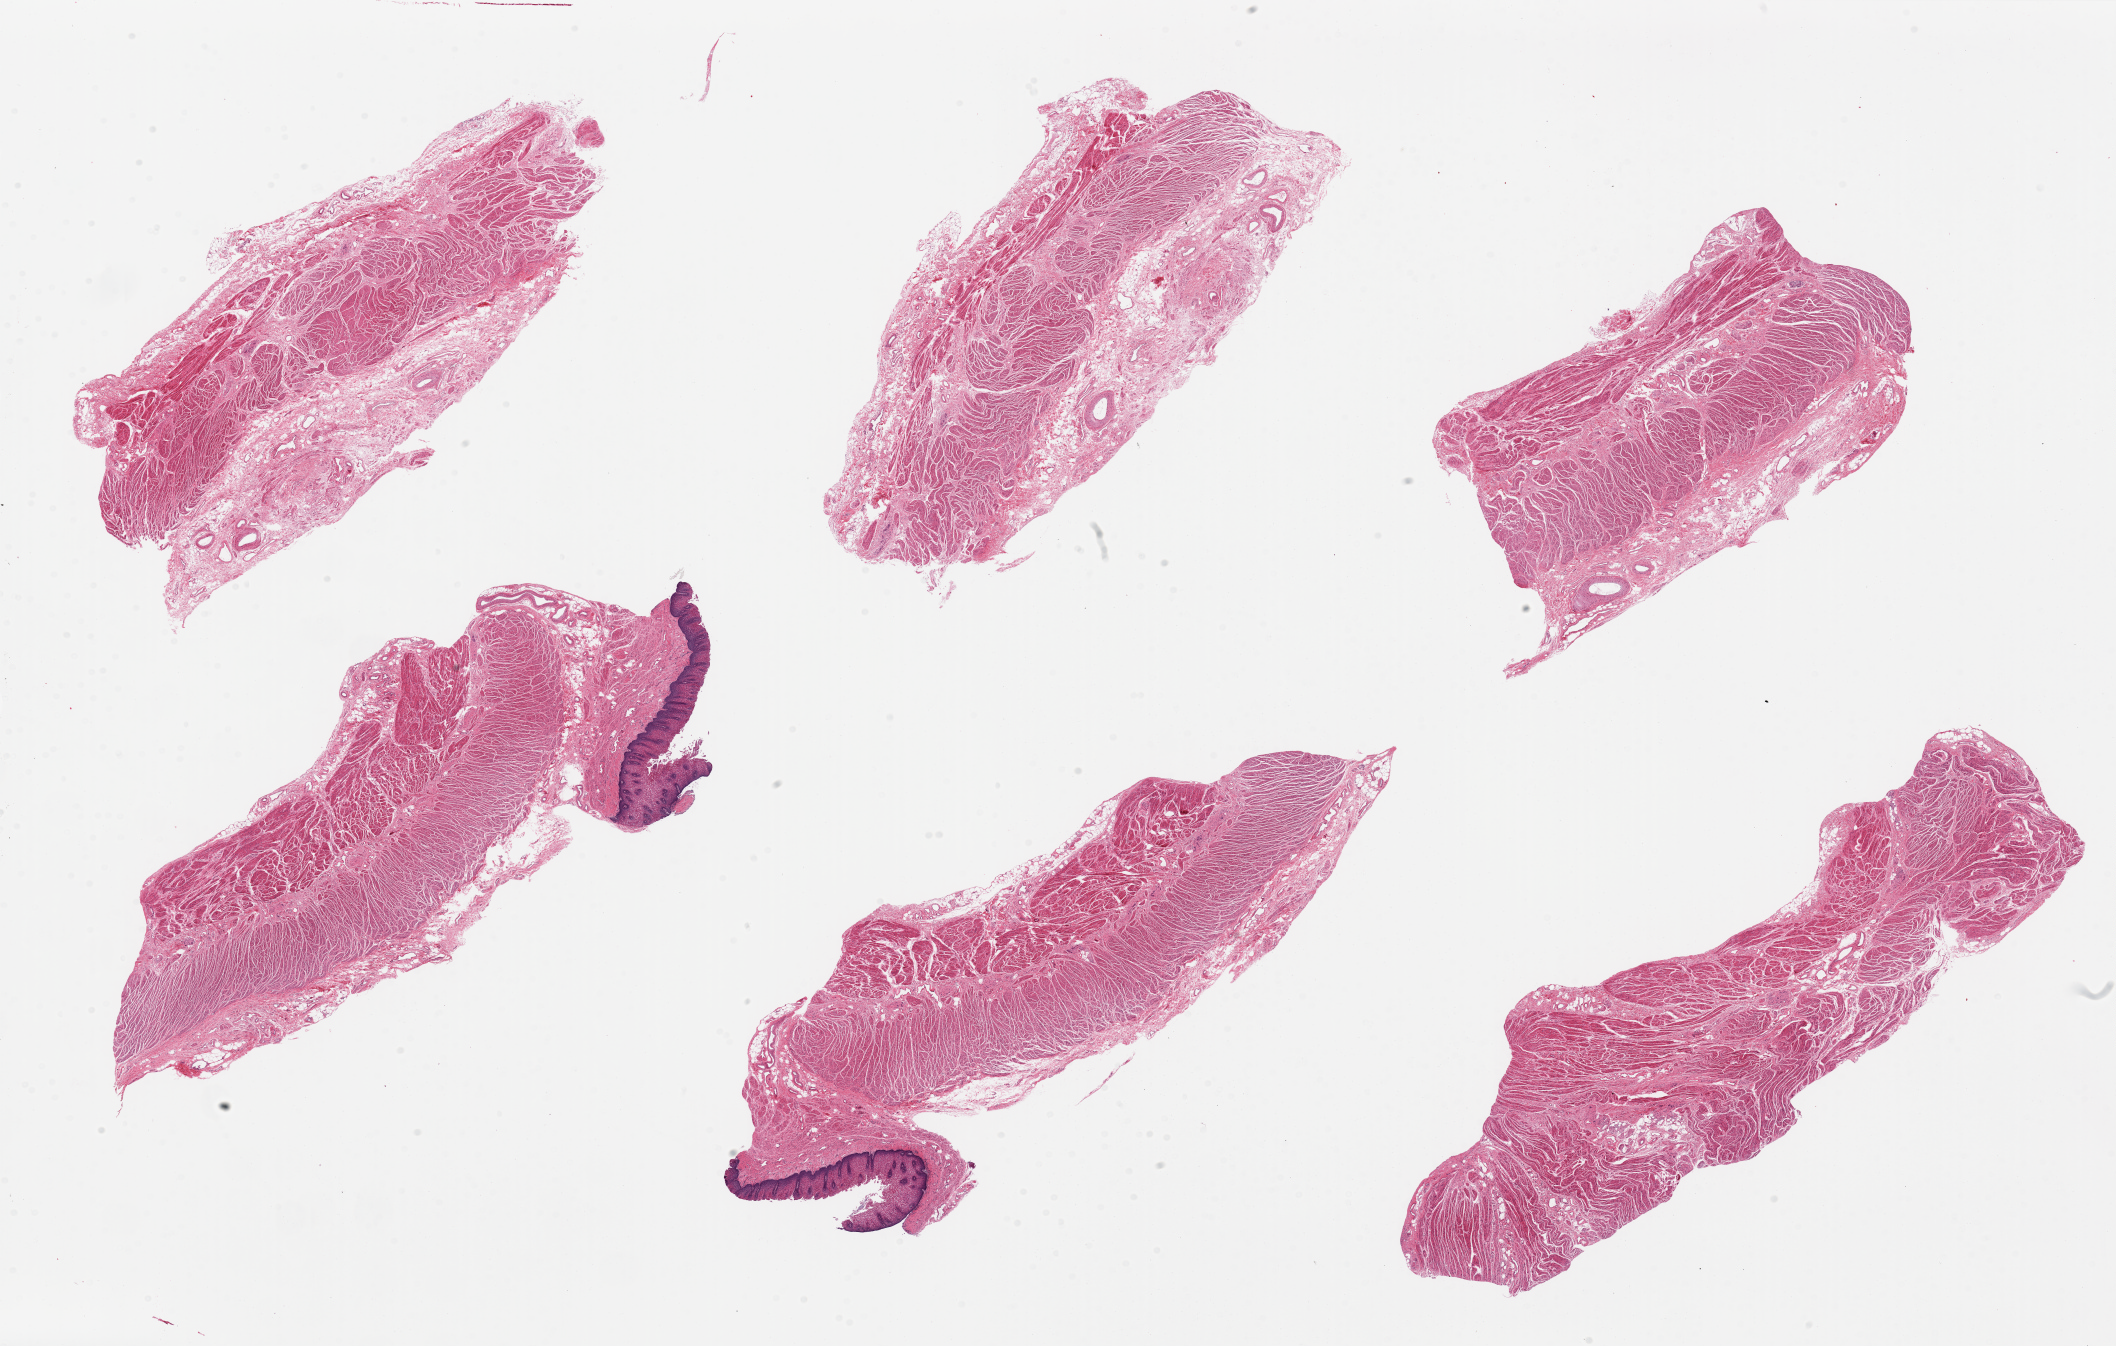
Digitized H&E-stained section — shown as a low-resolution overview of the whole scanned area (about 33.5 x 21.3 mm), PAXgene-fixed paraffin-embedded (PFPE) section, section of gastroesophageal junction (target tissue), donor tissue sample. Donor sex: male.
Reviewer comment on this tissue sample: 6 pieces; 2 pieces have [4 mm] squamous epithelium [ NOT target]; muscle present in all 6.